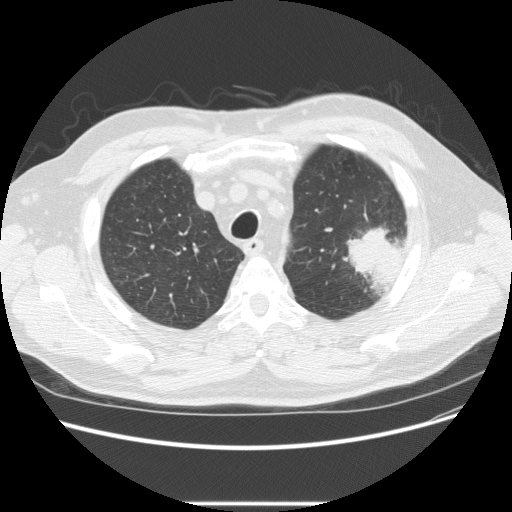
Low-dose screening chest CT, one axial slice. Position 183 of 233 along the scan axis. Reconstruction kernel STANDARD. Lung window (W 1500 / L -600 HU). 2.5 mm slice thickness. 512 × 512 image matrix, field of view 380 × 380 mm.
Outlined on this slice (expert manual segmentation):
- lesion 1 (tumor, upper lobe of left lung): bounding box <342,222,402,295> (left, top, right, bottom; pixels)